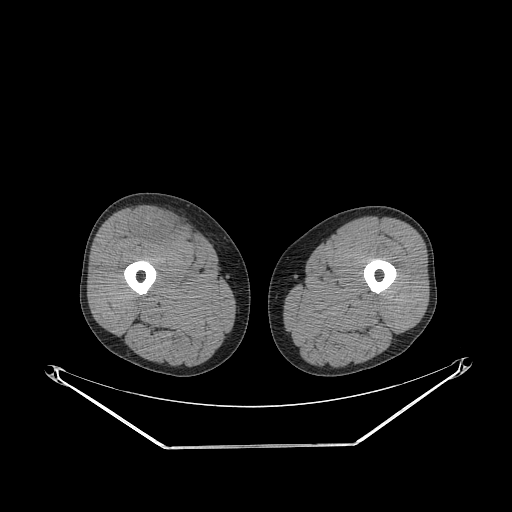
CT of an extremity soft-tissue mass (from a PET/CT study), one axial slice. Slice 260 of 311 in the series (ordered by position). 140 kVp. Soft-tissue window (W 400 / L 40 HU). 3.75 mm slice thickness. 512 × 512 image matrix. Male patient. Case-level facts recorded for this patient, not image findings: histological type: pleiomorphic leiomyosarcoma; grade: intermediate; site of the primary tumour: right thigh.
Structures marked on this image (expert contour drawn on MRI and transferred to this co-registered scan by the dataset authors):
- gross tumour volume including surrounding oedema: box from (x=132, y=210) to (x=179, y=241) px